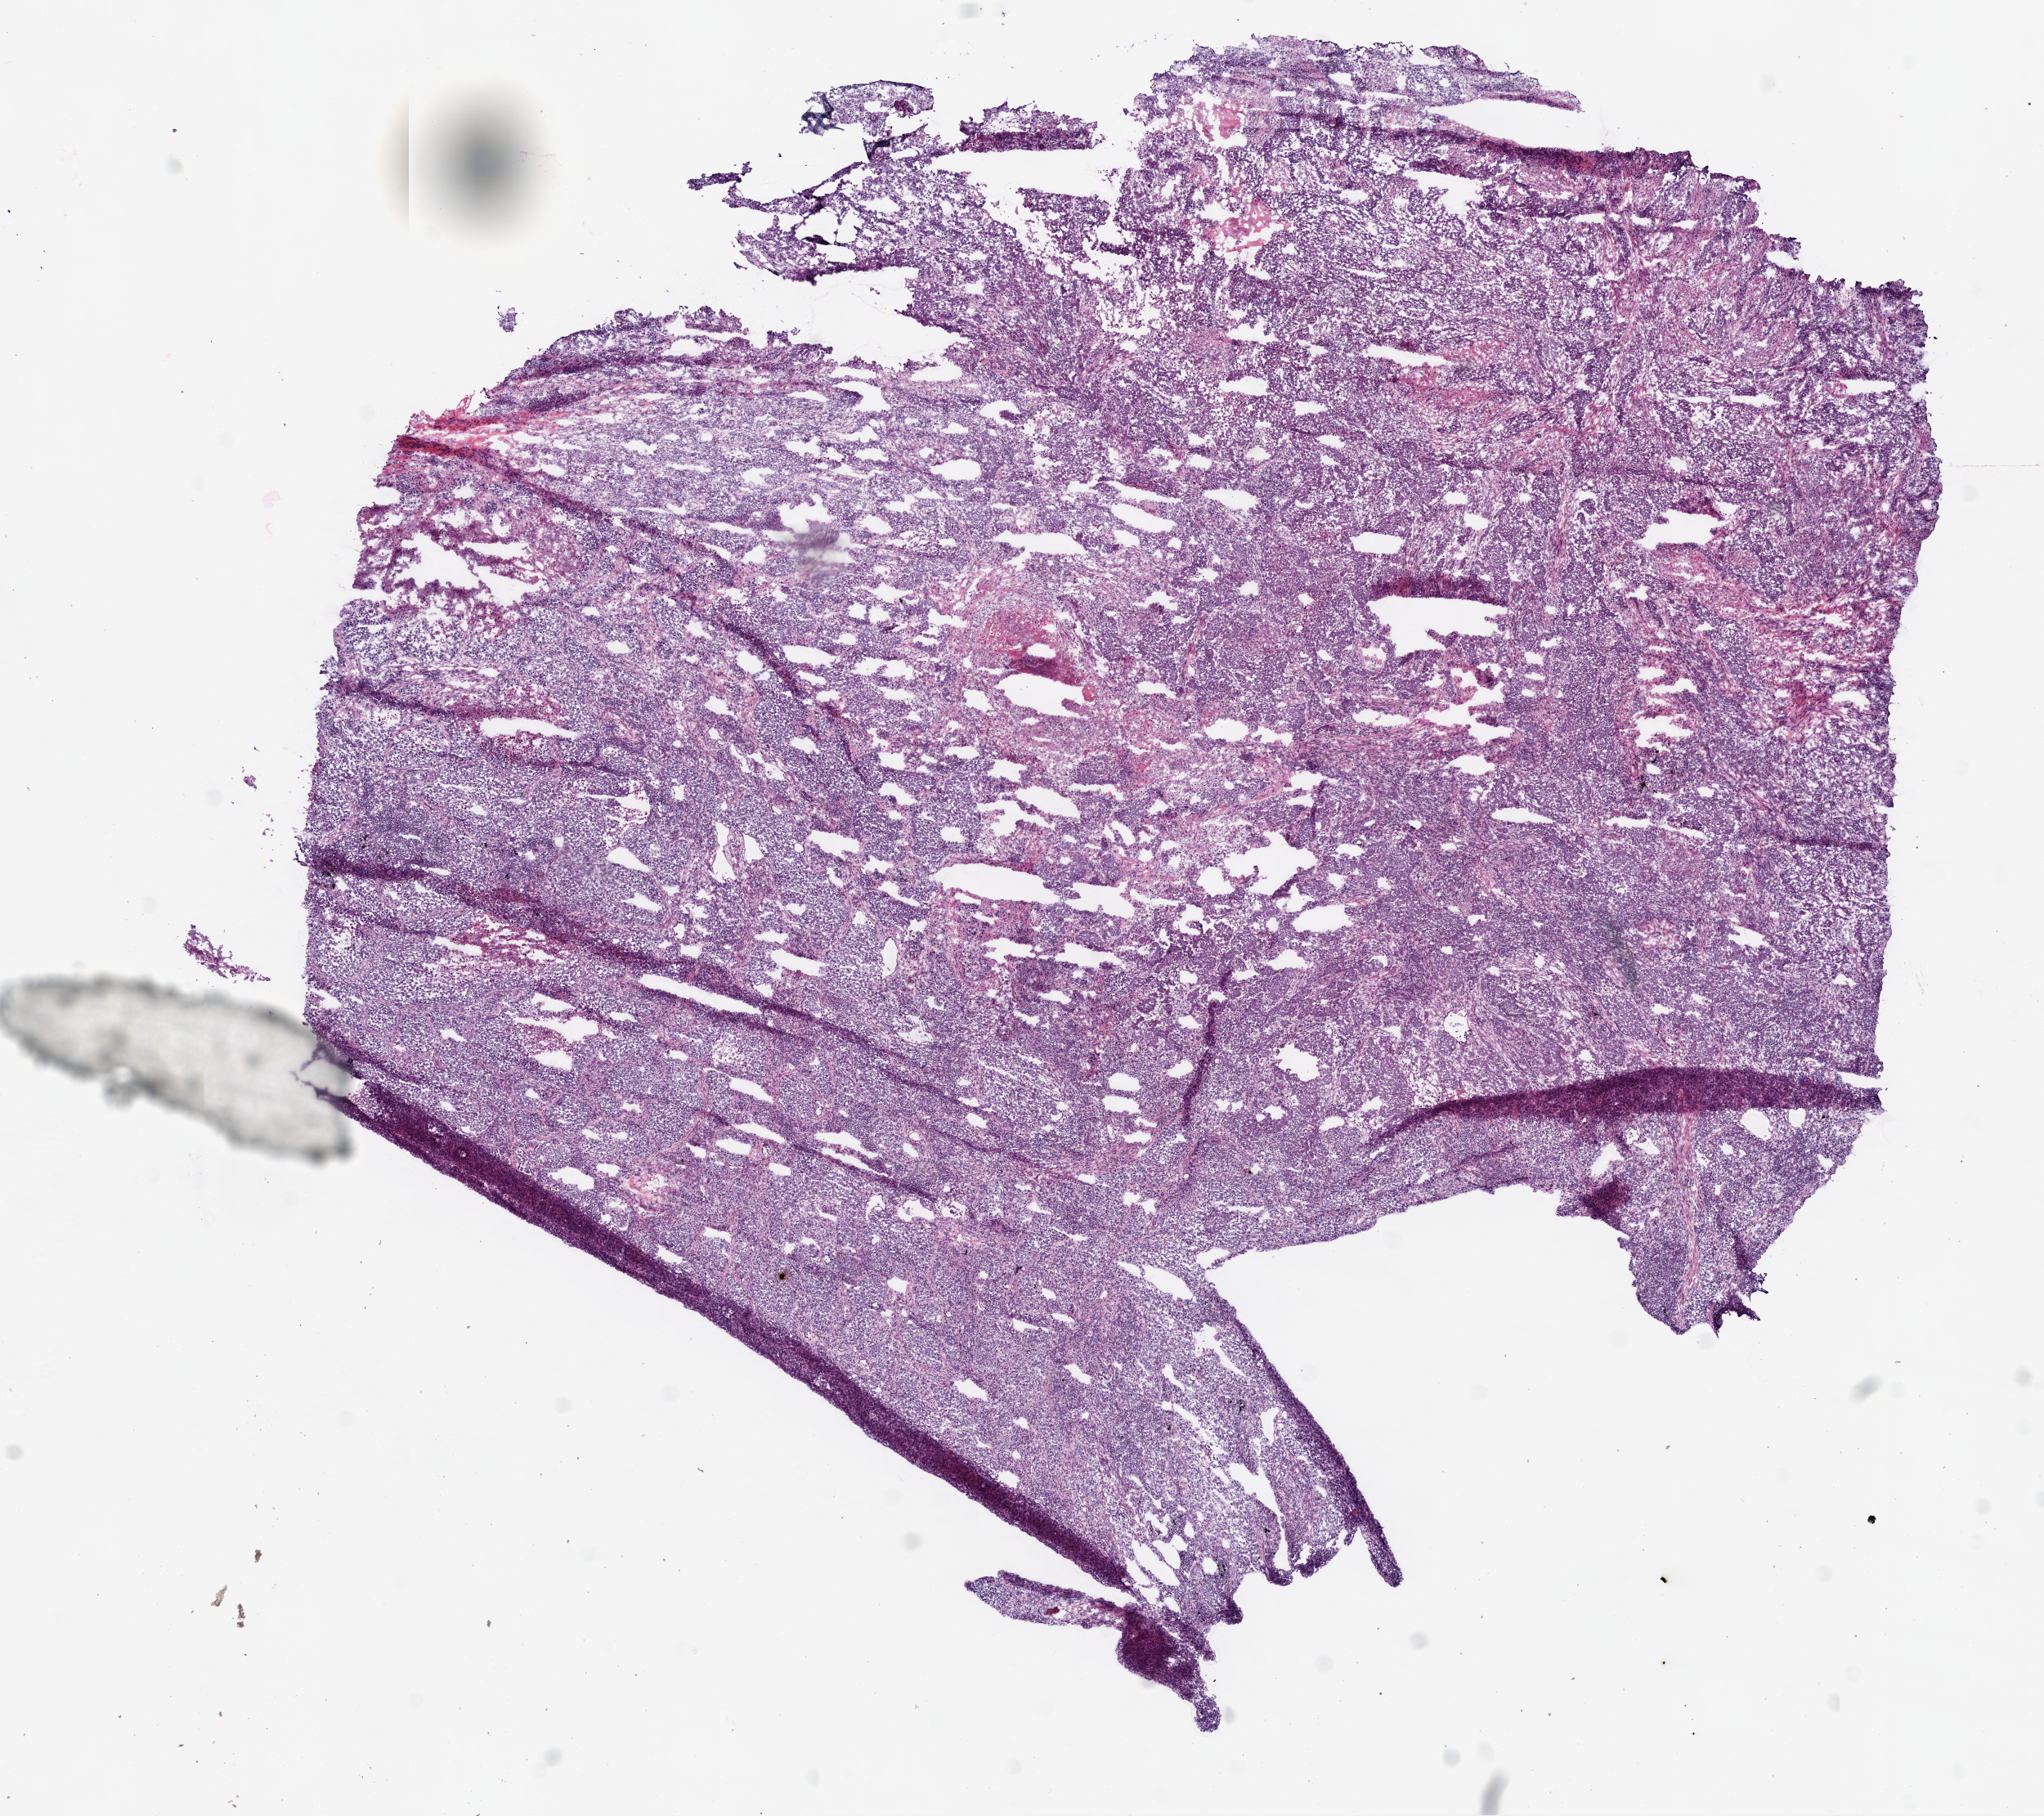
Digitized Hematoxylin and eosin (H&E) stained tissue section (whole slide) — a low-resolution overview of the entire scanned area, about 10.0 x 8.9 mm (slide scanned at 20x); frozen section from the bottom of the tissue portion; sample: primary tumour, lung. Male, age 66 years at initial diagnosis.
Histologic diagnosis: Squamous cell carcinoma, NOS (lower lobe, lung).